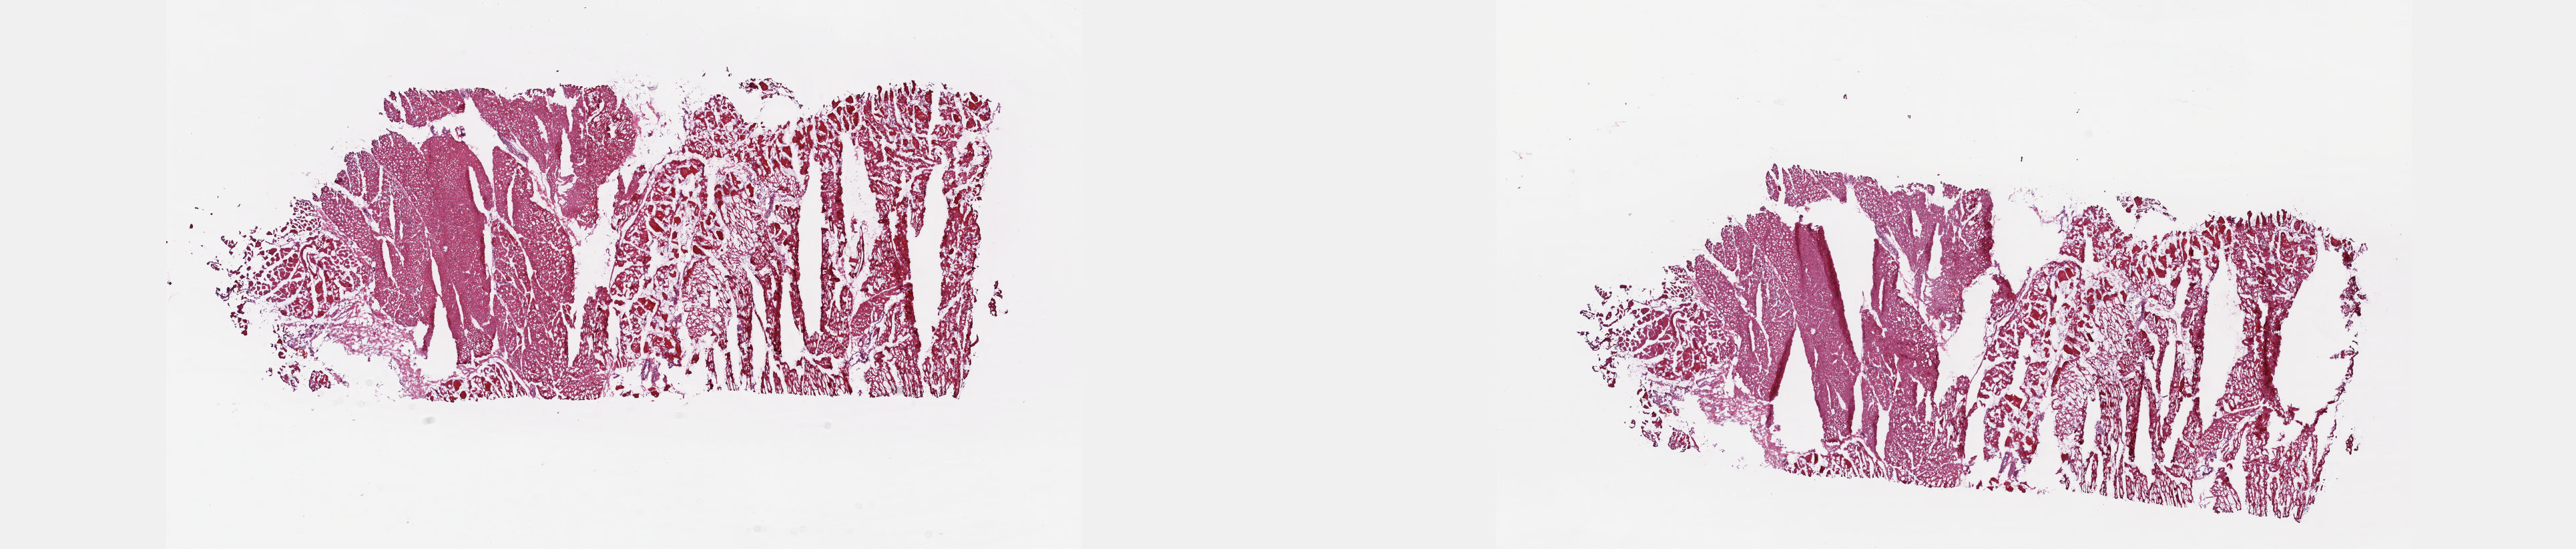
Digitized H&E-stained tissue section (whole slide), whole scanned area (about 31.1 x 6.6 mm, from a 20x scan) shown as a low-resolution overview; frozen section; solid tissue normal (non-tumour tissue) sample from the connective, subcutaneous and other soft tissues. Female, age 78 years at initial diagnosis. Composition of this section per pathologist review: tumour cells 0%, tumour nuclei 0%, normal cells 100%, stromal cells 0%, necrosis 0%. Inflammatory infiltration, as recorded: lymphocyte infiltration 1%, monocyte infiltration 0%, neutrophil infiltration 0%.
• this section: solid tissue normal (non-tumour) sample from the same patient
• patient diagnosis: Undifferentiated sarcoma